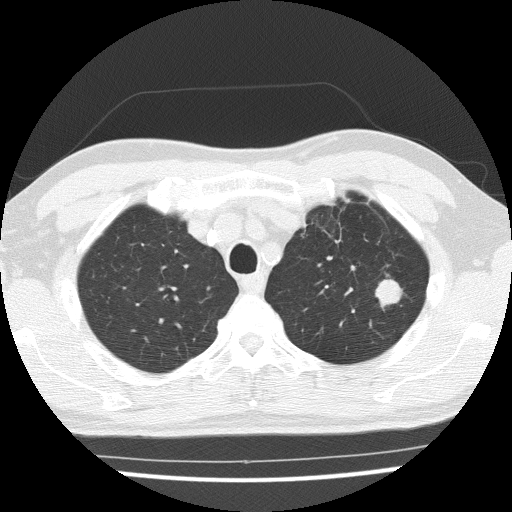
Low-dose screening chest CT, one axial slice. Slice 120 of 154 in the series (ordered by position). Reconstruction kernel FC51. 120 kVp. Lung window (W 1500 / L -600 HU). 512 × 512 image matrix, field of view 330 × 330 mm.
Annotated regions visible in this slice (outlined manually by an expert reader):
- lesion 1 (tumor, upper lobe of left lung): bounding box [x1, y1, x2, y2] px = [176, 279, 402, 308]